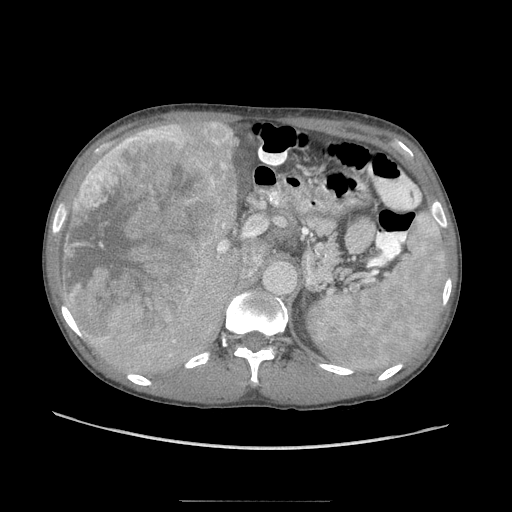
Contrast-enhanced abdominal CT (liver protocol), one axial slice; slice 55 of 103 in the series (ordered by position); 120 kVp; soft-tissue window (W 400 / L 40 HU); 2.5 mm slice thickness; 512 × 512 image matrix. Case-level facts recorded for this patient, not image findings: diagnosis: hepatocellular carcinoma (patient treated with transarterial chemoembolisation; whether this scan precedes or follows treatment is not stated here); TNM stage (as recorded): Stage-IIIA; Child-Pugh class: A; tumour differentiation: moderately differentiated; tumour size: 16 cm.
Annotated regions visible in this slice (semi-automatic segmentation, software-assisted and operator-edited):
- liver parenchyma outside the tumour (the mass and vessels are separate outlines, so this box may not span the whole liver): bounding box [x1, y1, x2, y2] px = [60, 120, 240, 376]
- mass: [62, 120, 240, 344]
- liver vessels: [87, 138, 220, 257]